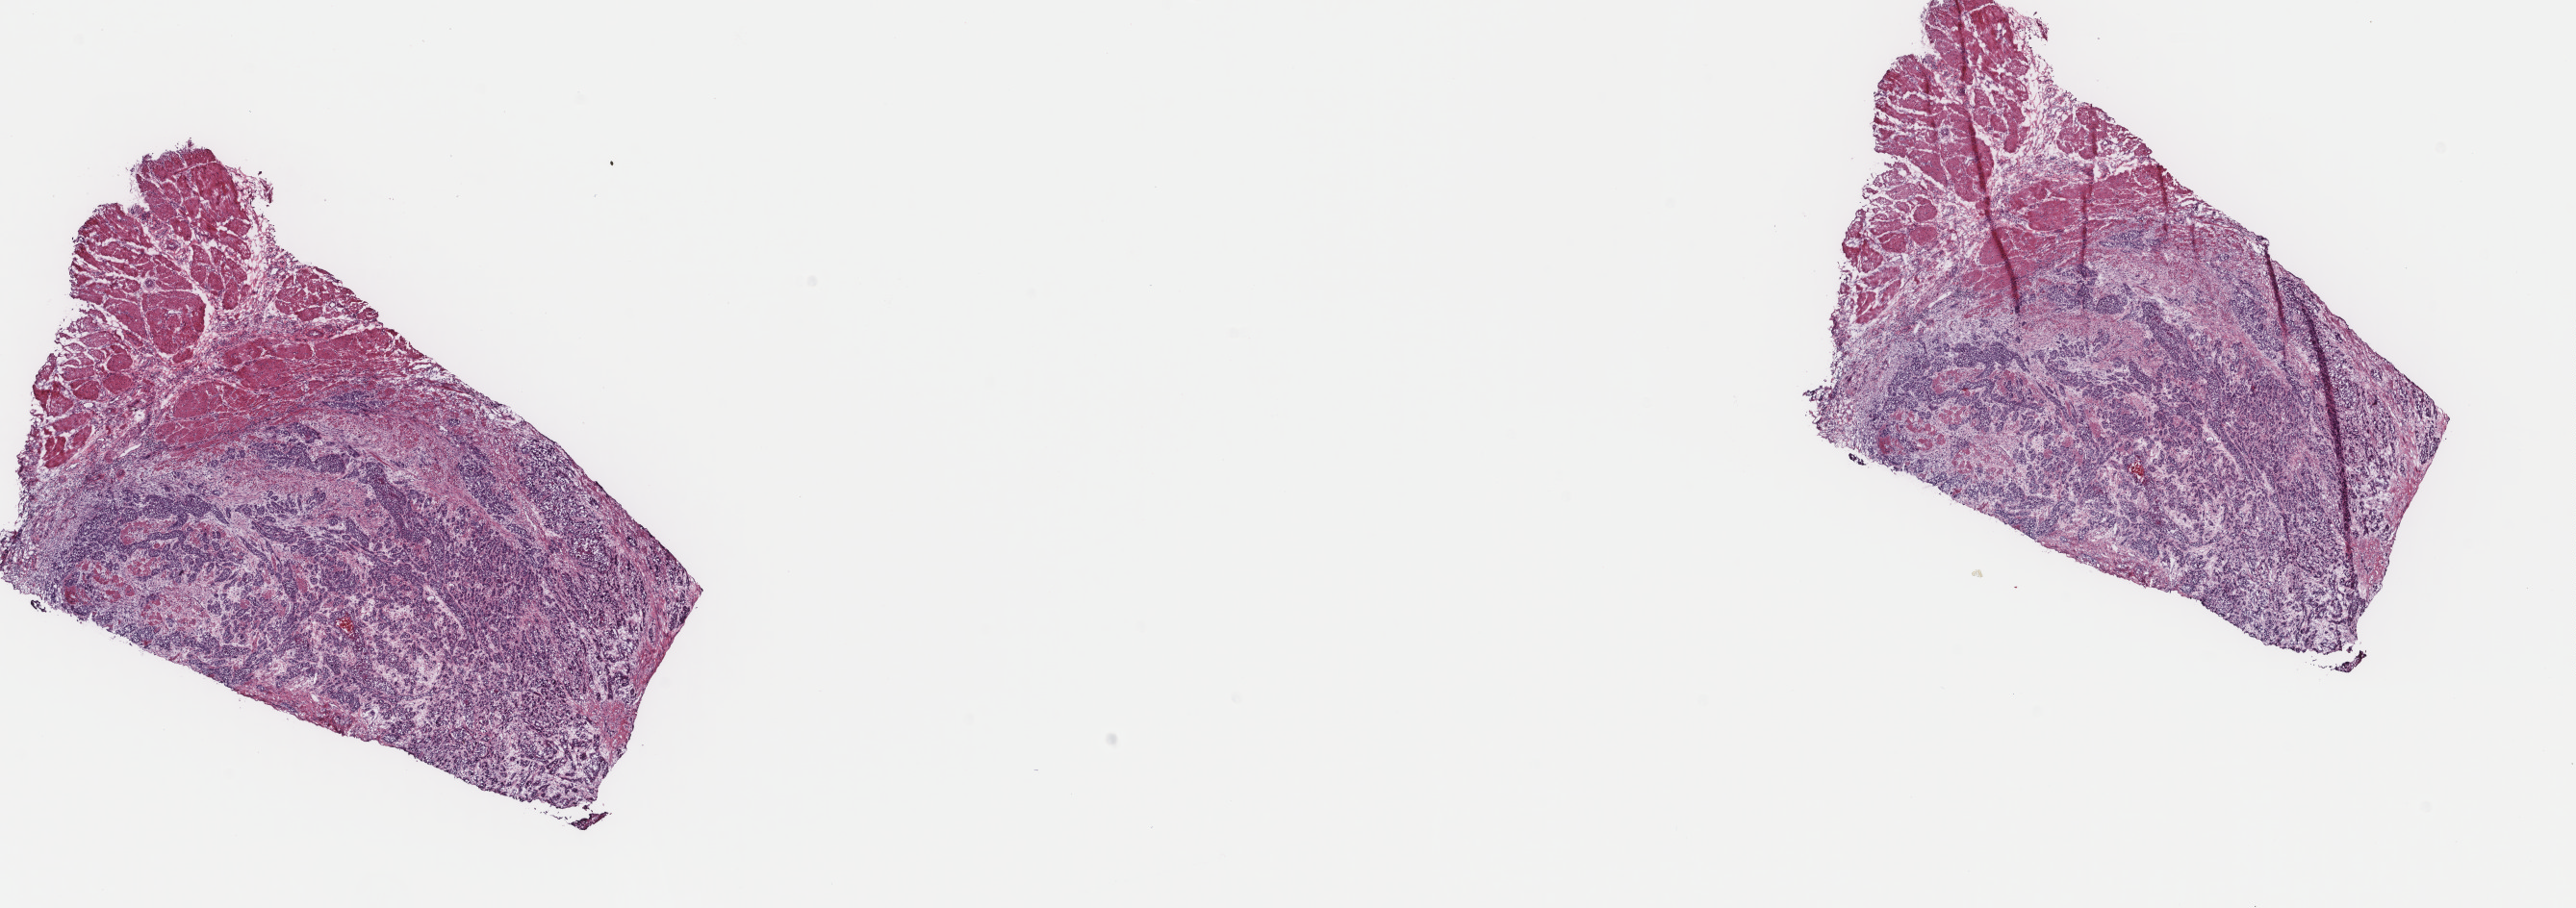
Whole-slide histology image, H&E-stained — a low-resolution overview of the entire scanned area, about 21.2 x 7.5 mm (slide scanned at 40x). Frozen section from the top of the tissue portion. Esophagus, primary tumour sample. Patient sex: male. Histologic grade: G3 (poorly differentiated). Slide review estimates, as recorded: tumour cells 70%, tumour nuclei 65%, normal cells 30%, stromal cells 0%, necrosis 0%. Inflammatory infiltration, as recorded: lymphocyte infiltration 2%, monocyte infiltration 0%, neutrophil infiltration 0%.
Pathologic diagnosis: Squamous cell carcinoma, NOS (middle third of esophagus). AJCC pathologic stage: IIB.